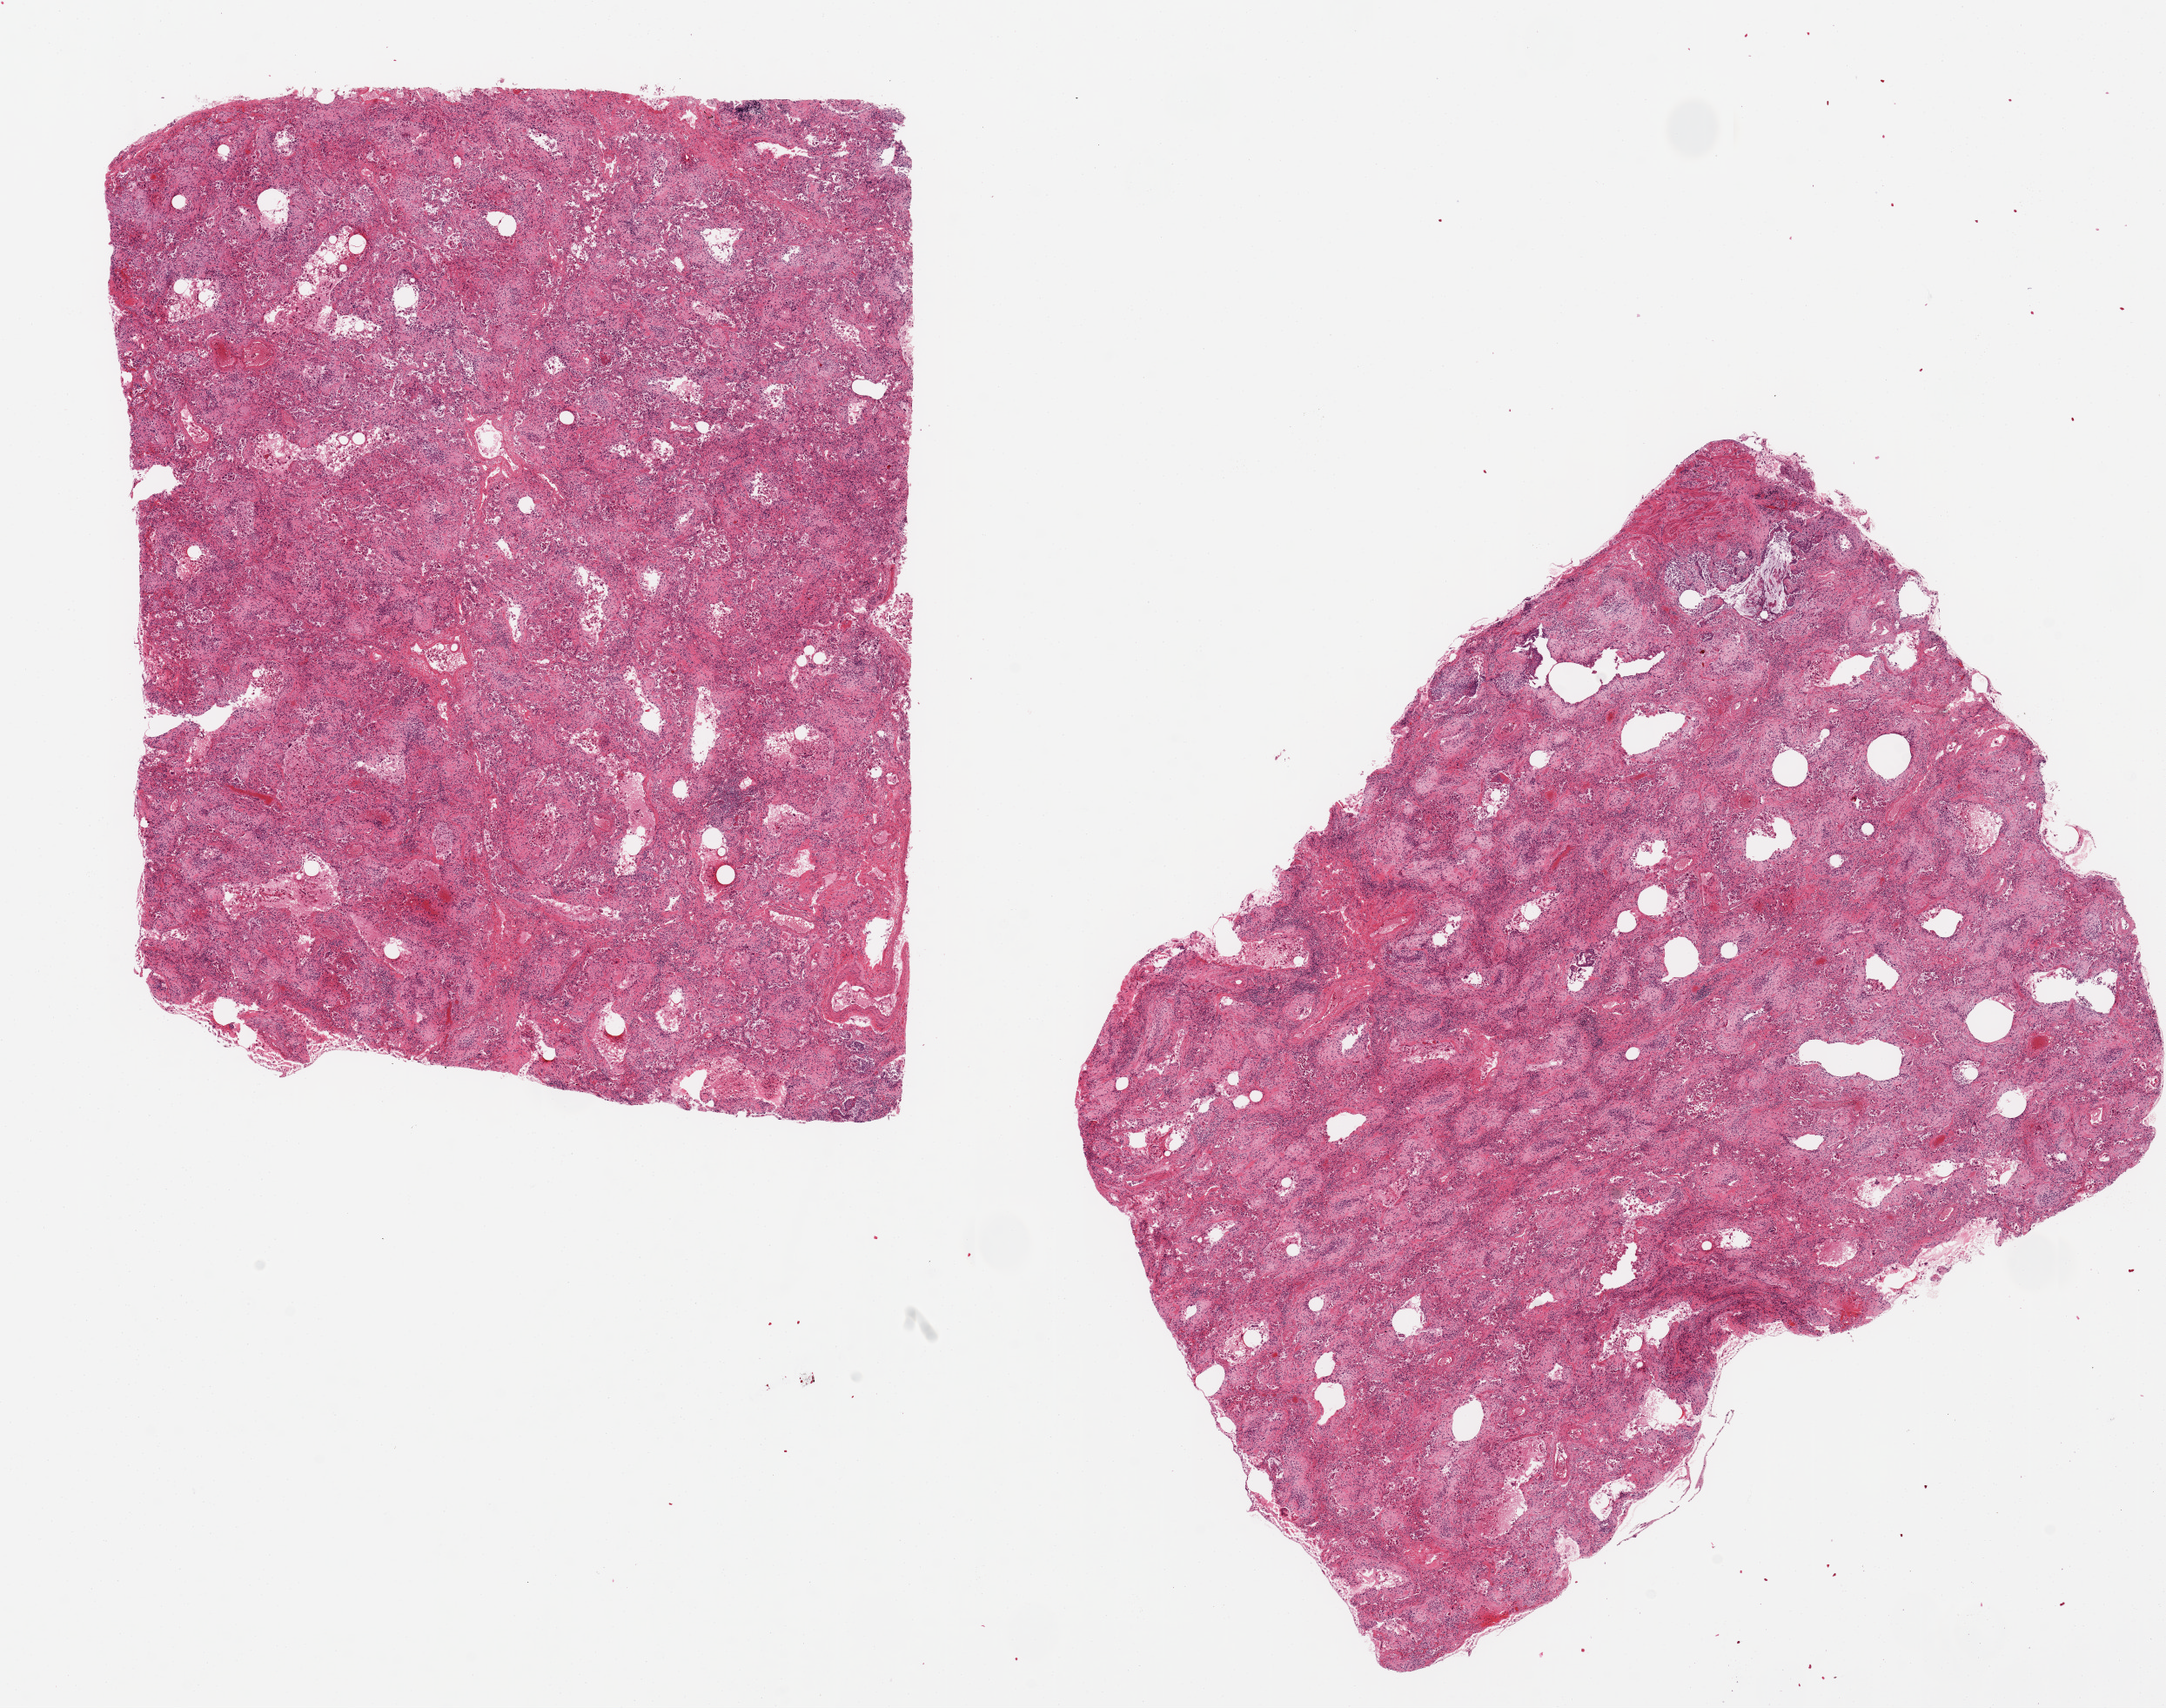
H&E whole-slide image, whole scanned area (about 19.7 x 15.5 mm) shown as a low-resolution overview, PAXgene-fixed paraffin-embedded (PFPE) section, target tissue: lung, tissue donor sample. Female donor.
Pathologist's review note for this sample: 2 9x7.5mm aliquots. Diffuse infiltrative process, suspect squamous carcinoma/fibrosis. Severe autolysis hampers evaluation; need slides to review.